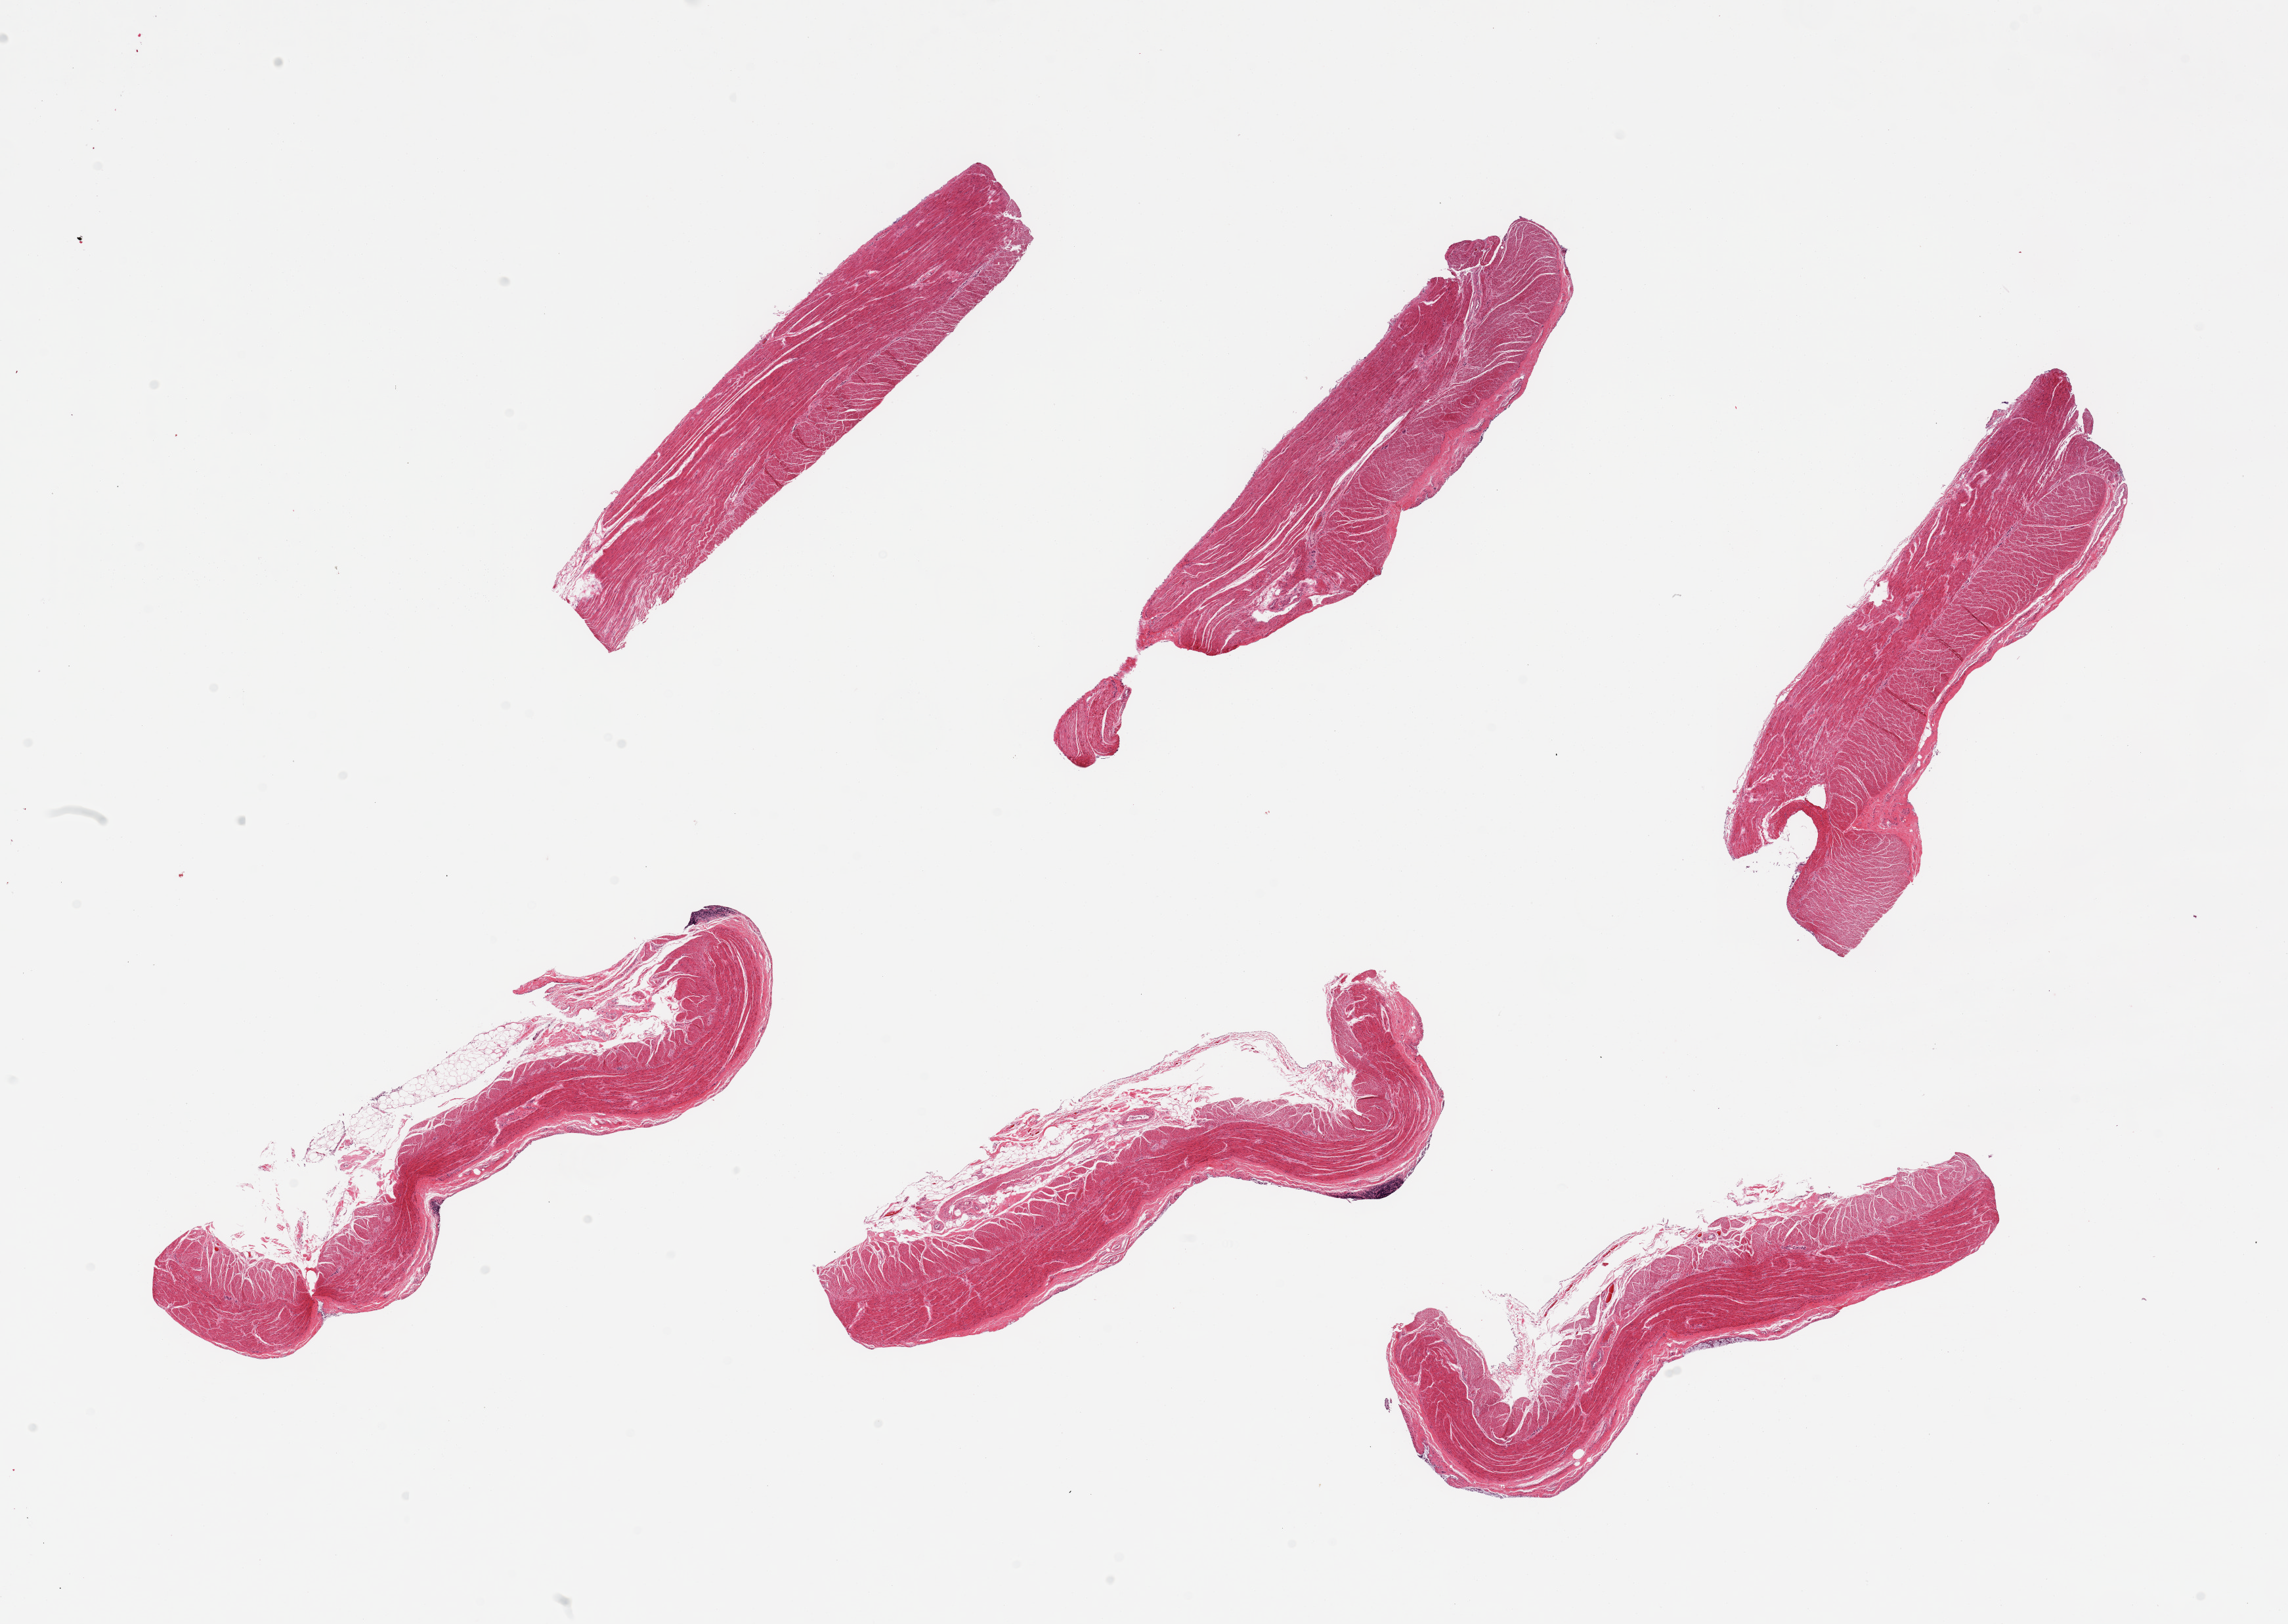
Hematoxylin and eosin (H&E) whole-slide image, shown as a low-resolution overview of the whole scanned area (about 27.6 x 19.6 mm), PAXgene-fixed, paraffin-embedded tissue, sampled site (target tissue): sigmoid colon, donor tissue sample. Female donor.
Review note (as recorded): 6 pieces, predominantly well trimmed with scant residual mucosa.